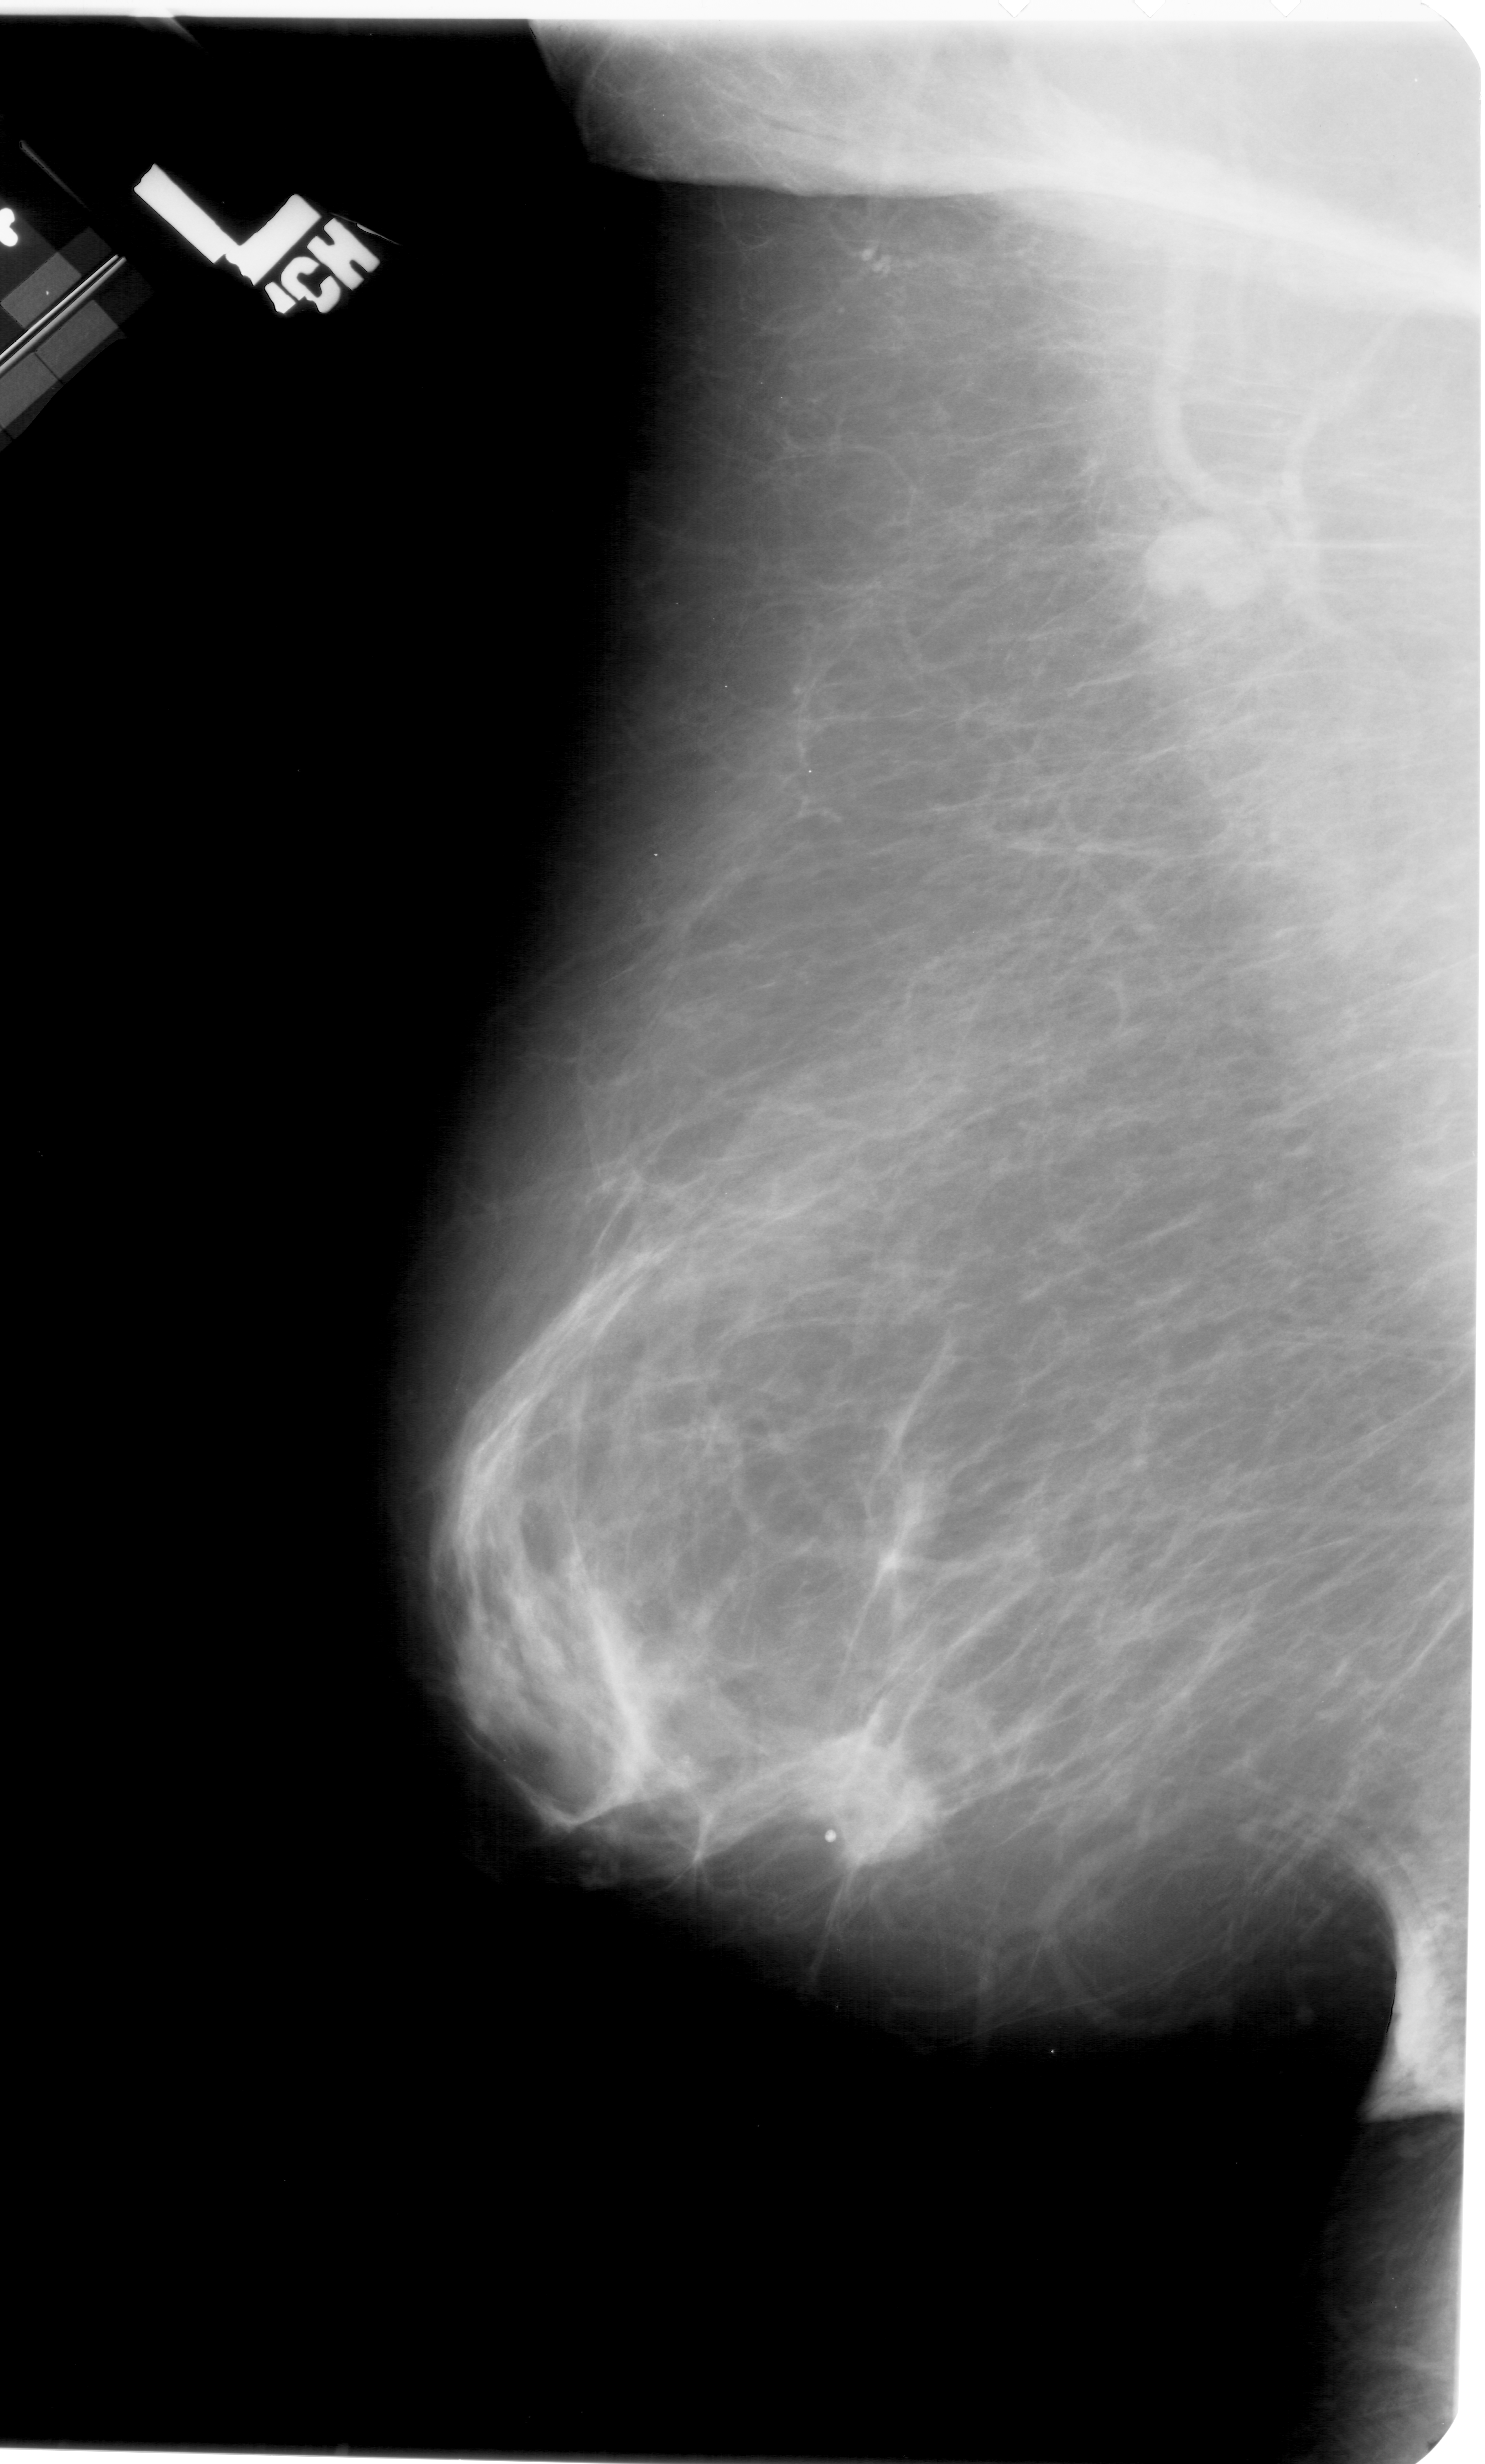
Mammogram (digitized film); left breast; MLO view; breast composition: almost entirely fatty (BI-RADS density category 1 of 4); 1485 × 2464 image matrix.
Expert-marked regions of interest on this image (one box per marked abnormality):
- mass, shape oval, margins spiculated; BI-RADS assessment category 5; subtlety rating 5 on a 1 (subtle) to 5 (obvious) scale; pathology (as recorded): malignant: box from (x=780, y=1666) to (x=1008, y=1907) px